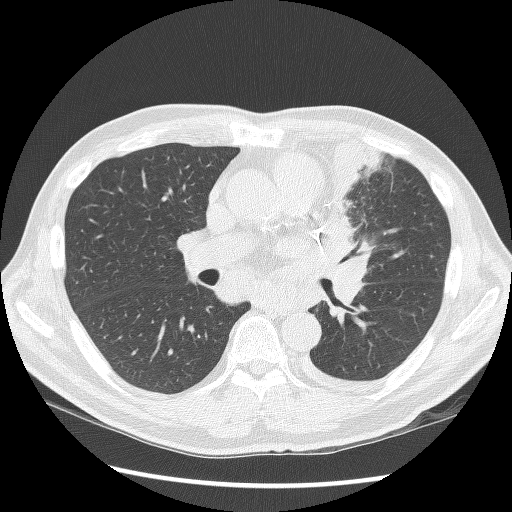
Low-dose screening chest CT, axial slice, second annual screen, lung window (W 1500 / L -600 HU), lung (sharp) reconstruction kernel (BONE), 512 × 512 image matrix, field of view 360 × 360 mm. Male participant, aged 64 years at enrolment. Former smoker at enrolment.
Expert-annotated lung lesion, box from (x=305, y=132) to (x=392, y=279) px. Screening reader's record for this exam: no non-calcified nodule ≥4 mm recorded. Official screen result: positive, other. Participant outcome: lung cancer diagnosed 24 days after this screen — small cell carcinoma, NOS, left upper lobe, stage IV (AJCC 6th edition), 100 mm at pathology.